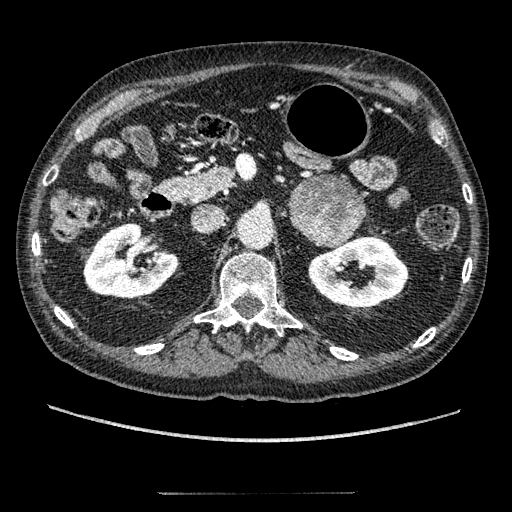
Contrast-enhanced abdominal CT, one axial slice. Slice 113 of 274 in the series (ordered by position). Reconstruction kernel STANDARD. Intravenous contrast given. Soft-tissue window (W 400 / L 40 HU). 1.25 mm slice thickness. 512 × 512 image matrix, field of view 381 × 381 mm. Patient: male, 69 years. Case-level facts recorded for this patient, not image findings: diagnosis: adrenocortical carcinoma; tumour side: left adrenal; tumour size at pathology: 6.1 cm; Ki-67 index: 10 %; stage (as recorded): 3.
Annotated regions visible in this slice (semi-automatic segmentation, software-assisted and operator-edited):
- mass: bounding box [x1, y1, x2, y2] px = [292, 175, 365, 247]